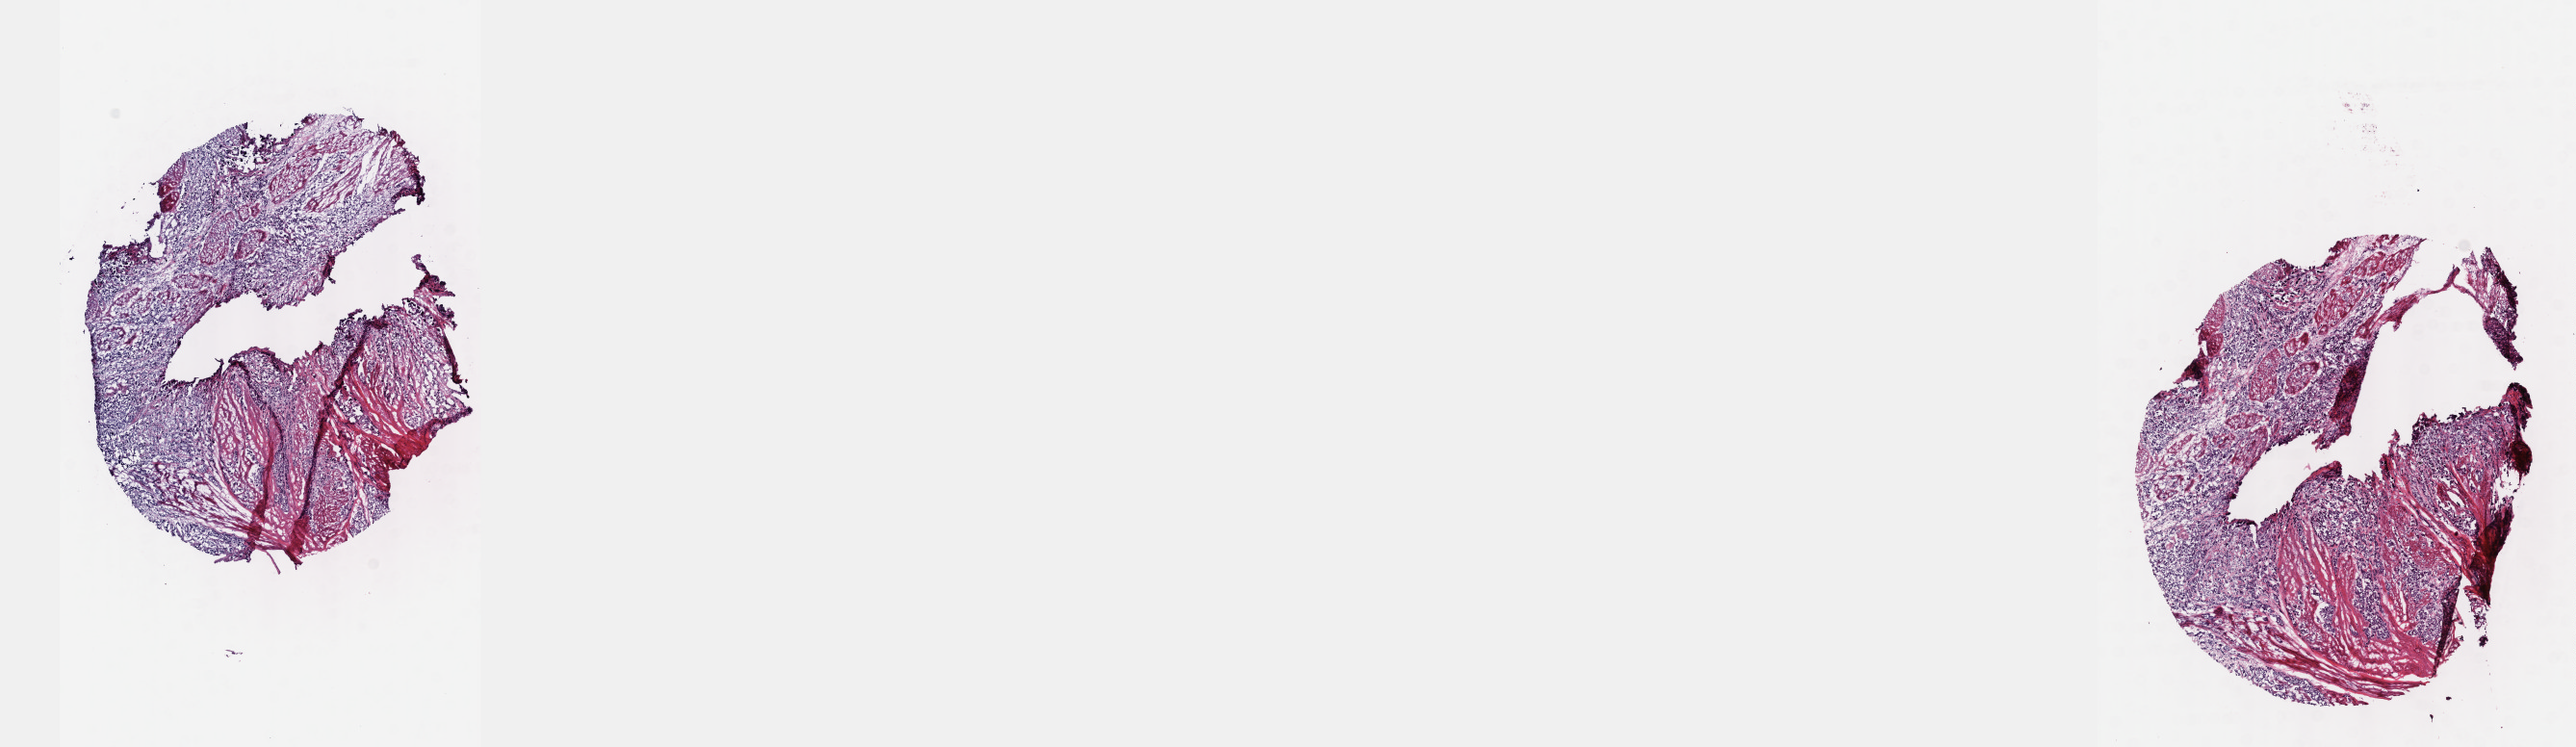
H&E whole-slide image — a low-resolution overview of the entire scanned area, about 21.6 x 6.3 mm (acquisition: 40x scan), frozen section from the top of the tissue portion, primary tumour sample from the bladder. Patient: female, age at initial diagnosis 76 years. Histologic grade: high grade. Pathologist review of this section (percent, as recorded): tumour cells 80%, tumour nuclei 80%, normal cells 0%, stromal cells 19%, necrosis 1%. Inflammatory infiltration, as recorded: lymphocyte infiltration 2%, monocyte infiltration 1%, neutrophil infiltration 5%.
- AJCC pathologic stage: III
- histologic diagnosis: Transitional cell carcinoma